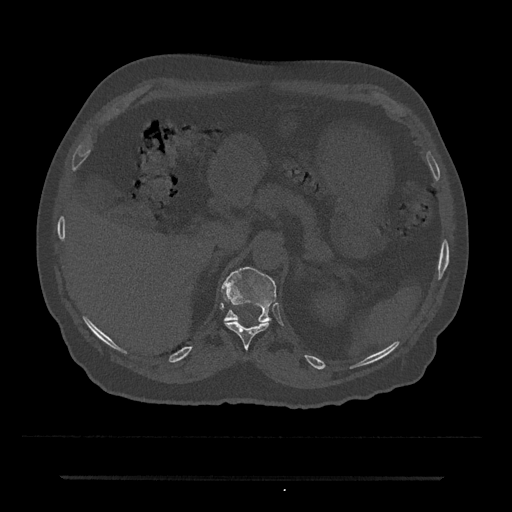
CT including the spine, one axial slice. 120 kVp. Bone window (W 1800 / L 400 HU). 0.5 mm slice thickness. 512 × 512 image matrix, field of view 437 × 437 mm. Patient: male, 69 years. Case-level facts recorded for this patient, not image findings: primary cancer: prostate.
Annotated regions visible in this slice (semi-automatically segmented with operator editing):
- T11 vertebra: bounding box [x1, y1, x2, y2] px = [225, 322, 269, 349]
- T12 vertebra: [223, 267, 276, 322]